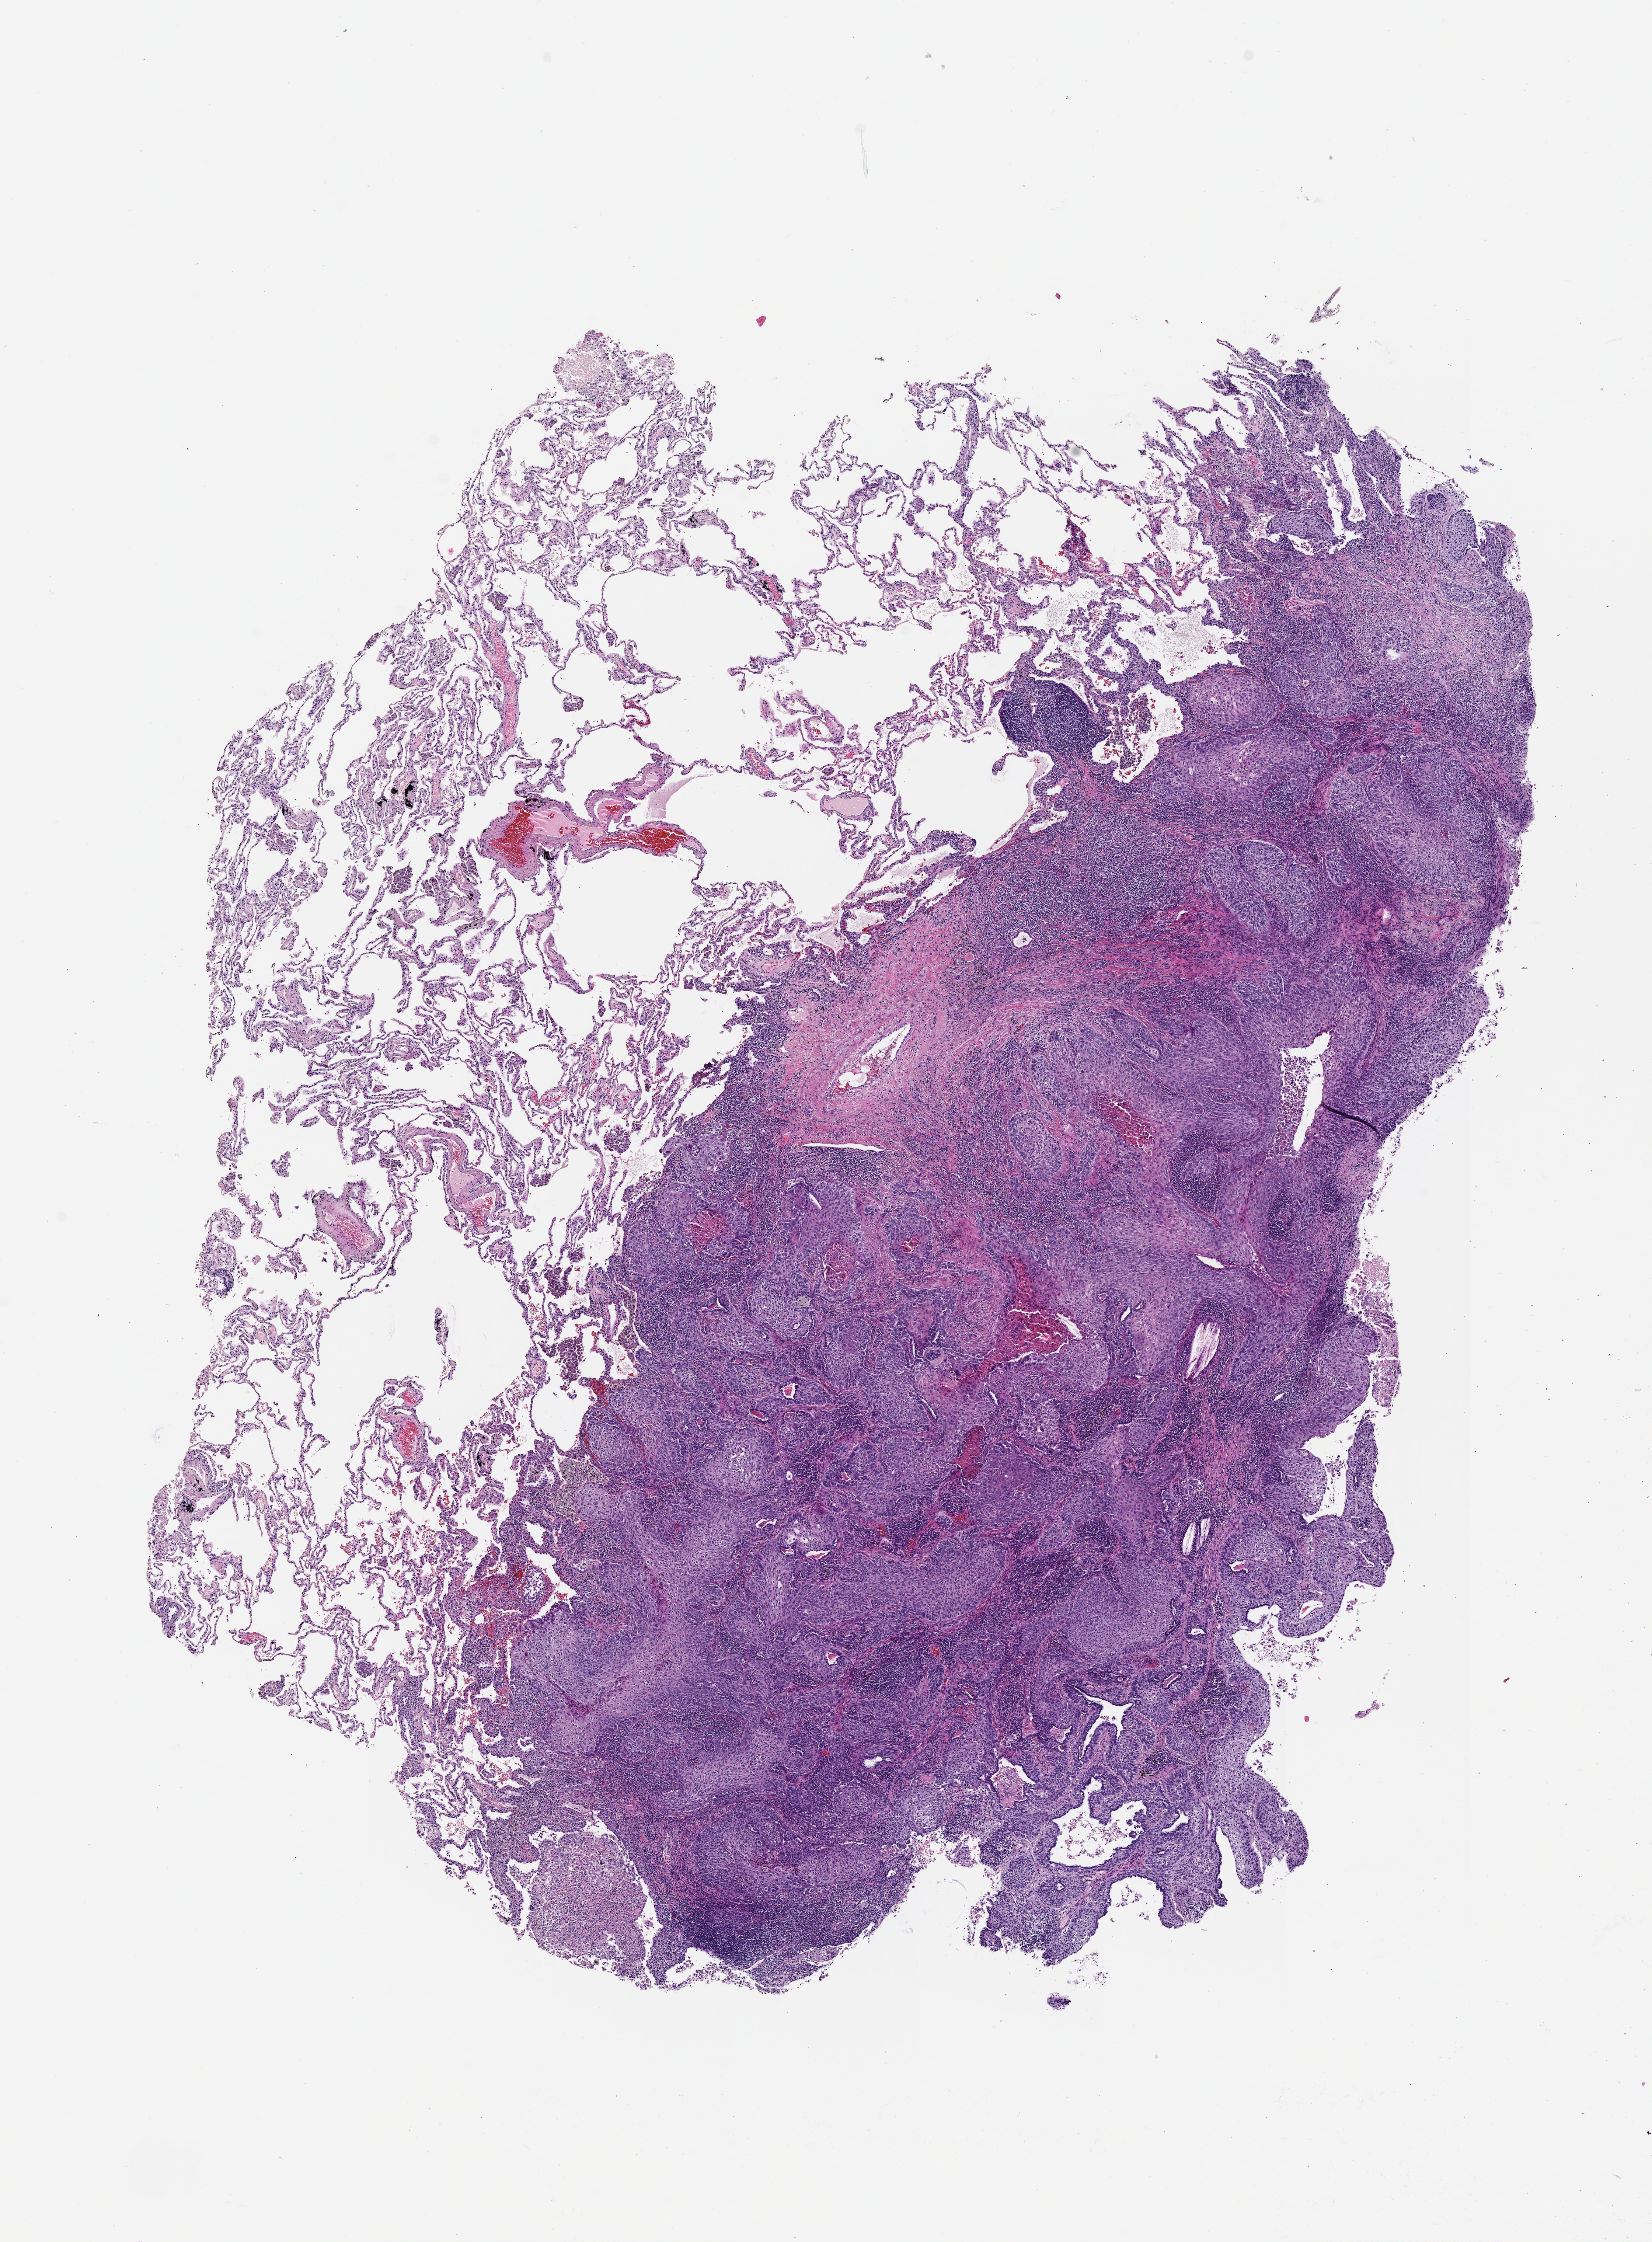
H&E-stained whole-slide image, low-resolution overview of the scanned area, about 9.0 x 12.2 mm; tumour tissue sample, lung. Male, 67 y/o.
Patient diagnosis (cohort enrolment): squamous cell carcinoma (lung).